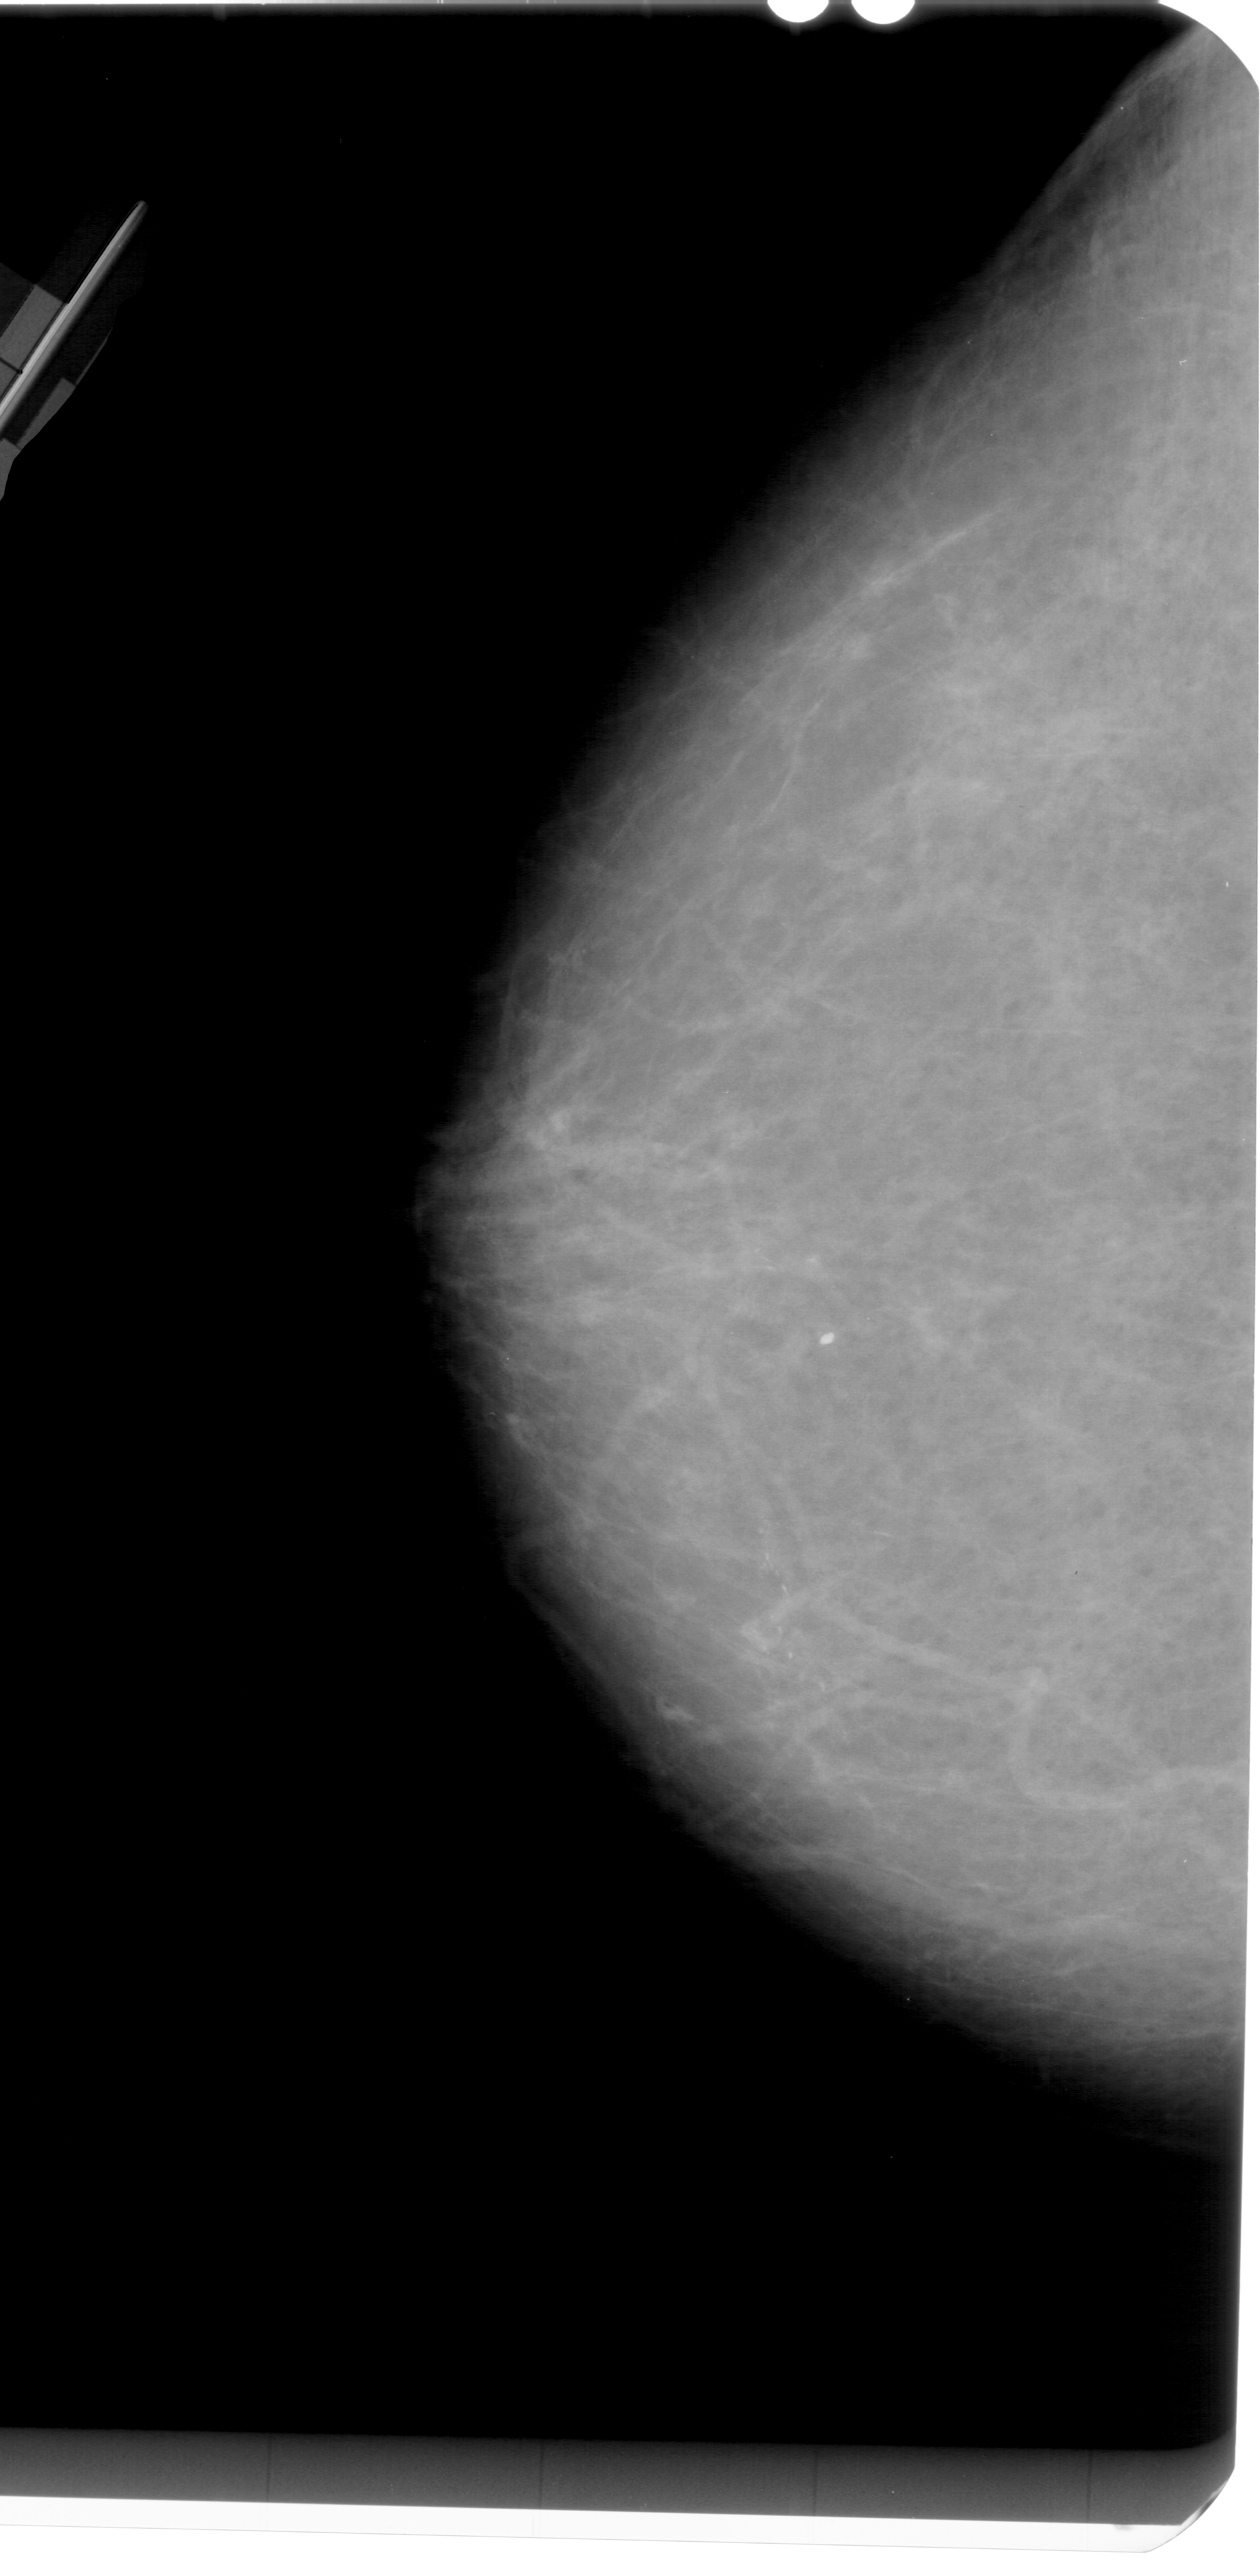
Scanned film-screen mammogram, left breast, CC view, BI-RADS breast density category 2 (scale 1–4).
Marked abnormality: calcifications, morphology pleomorphic, distribution linear; BI-RADS assessment category 4; pathology (as recorded): malignant.